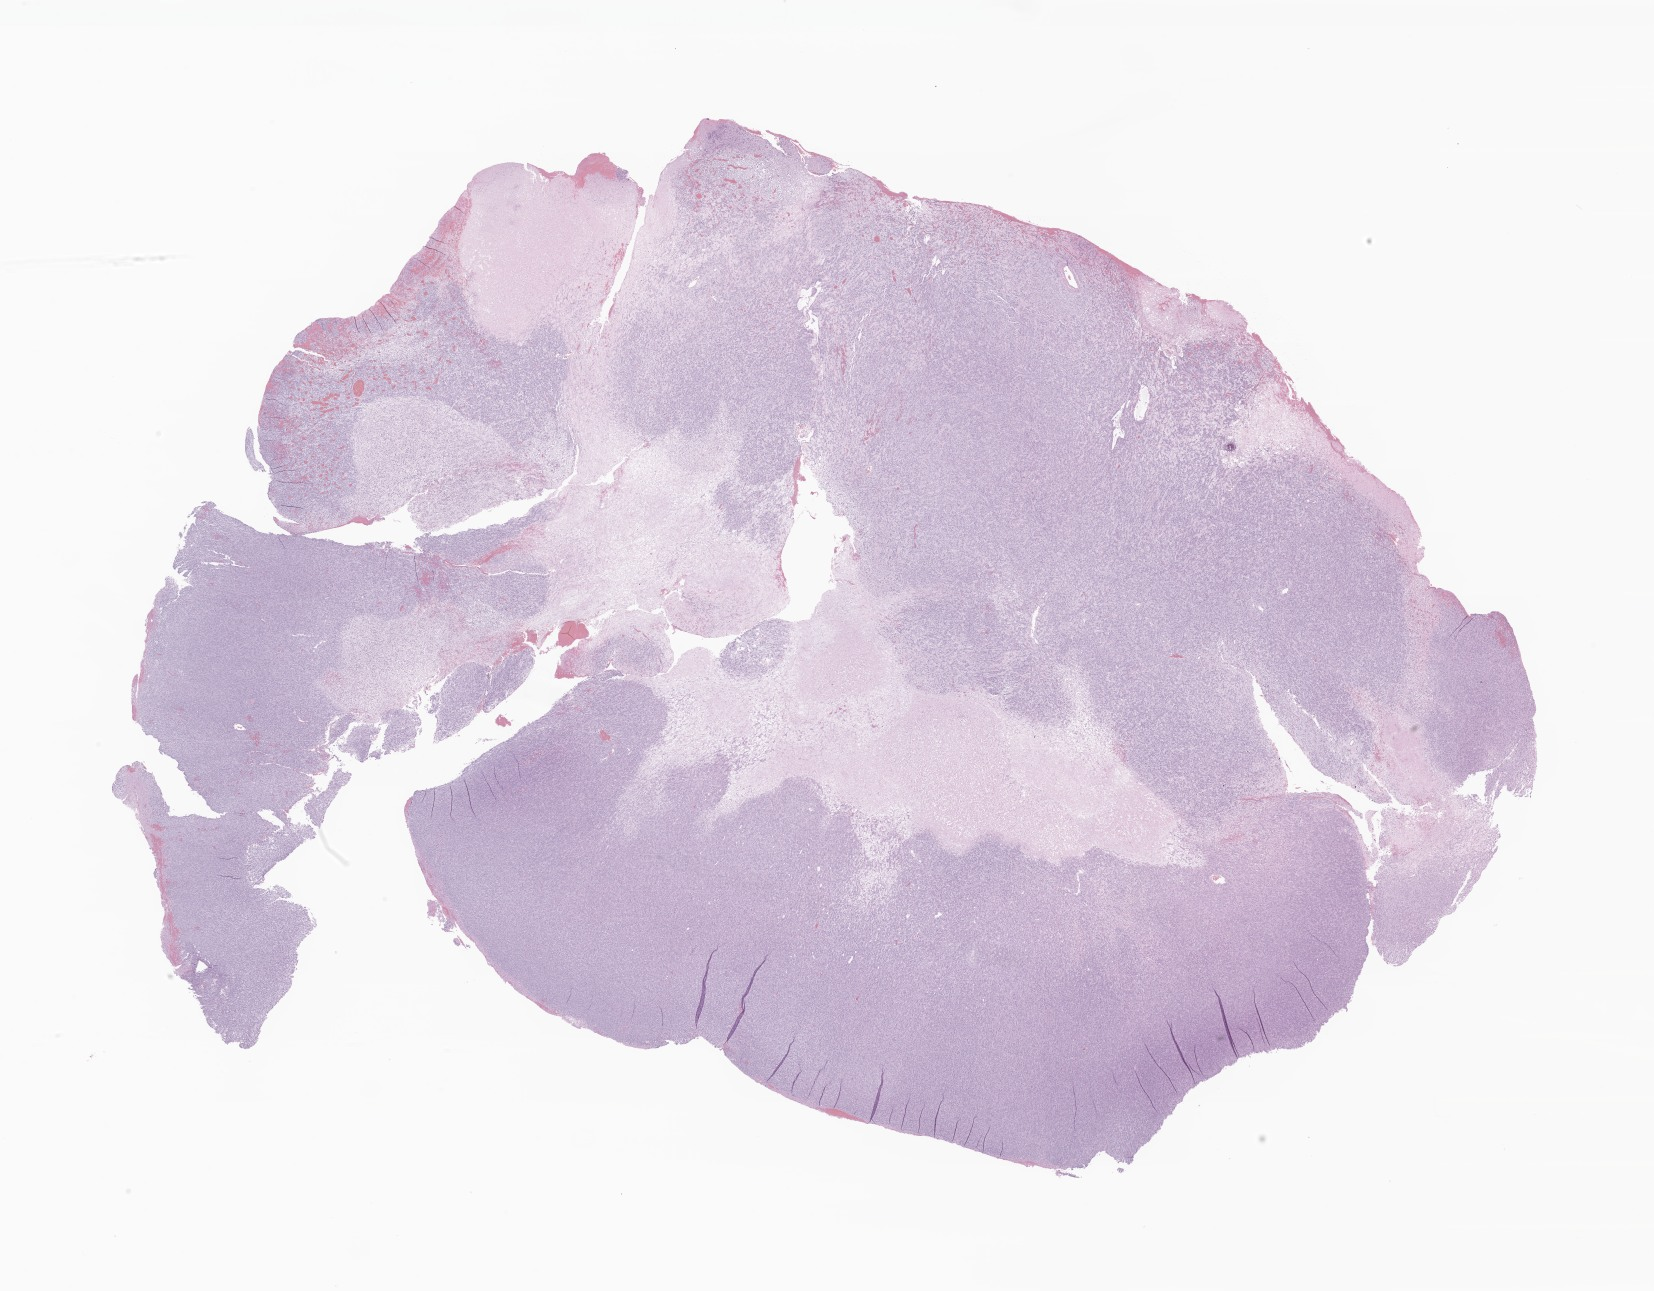
Haematoxylin and eosin whole-slide image of tumor tissue from the brain — a low-resolution overview of the entire scanned area, about 27.9 x 21.8 mm, FFPE section. Patient: male, age 86 months.
Recorded diagnosis: Astroblastoma.